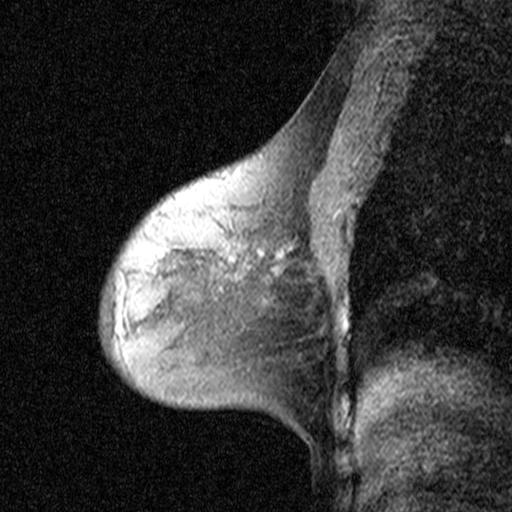
Breast MRI (dynamic contrast-enhanced), one sagittal slice. Position 27 of 44 along the scan axis. Dynamic contrast-enhanced study with each time point stored as its own series, time point 2 of 3 at this slice position (early post-contrast, ordered by acquisition time). 1.5 T. TE 4.5 ms, TR 11 ms. 3 mm slice thickness. 512 × 512 image matrix, field of view 200 × 200 mm. Patient: female, 53 years. From the clinical record (not read from this slice): setting: breast cancer imaged before/during neoadjuvant chemotherapy; receptor status: HR-positive, HER2-negative.
Outlined on this slice (semi-automatically segmented with operator editing):
- analysis volume of interest (the breast-tissue region the enhancement analysis was run in; not a lesion): bounding box [x1, y1, x2, y2] px = [186, 216, 307, 311]
- tumour enhancement mask (voxels above the 90 % enhancement threshold inside the analysis volume of interest): [224, 240, 281, 266]